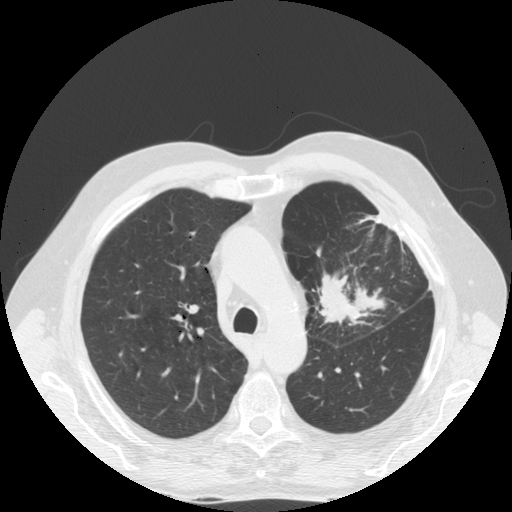
Low-dose screening chest CT, one axial slice. Position 122 of 170 along the scan axis. Reconstruction kernel STANDARD. Lung window (W 1500 / L -600 HU). 2.5 mm slice thickness. 512 × 512 image matrix, field of view 380 × 380 mm.
Annotated regions visible in this slice (expert manual segmentation):
- lesion 1 (tumor, upper lobe of left lung): box from (x=316, y=273) to (x=386, y=323) px